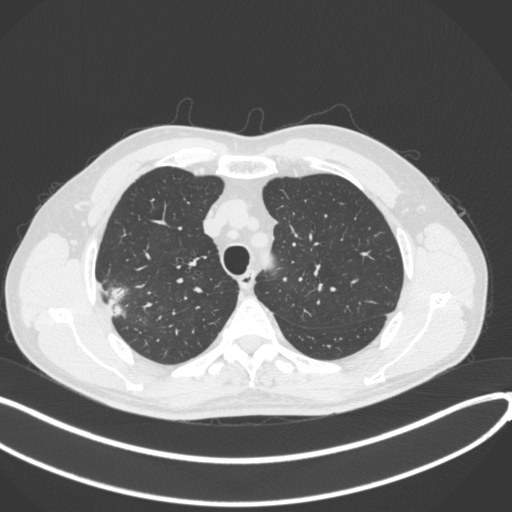
Chest CT, one axial slice; reconstruction kernel B31f; lung window (W 1500 / L -600 HU); 1 mm slice thickness; 512 × 512 image matrix, field of view 400 × 400 mm. Patient: male, 62 years. From the clinical record (not read from this slice): clinical TNM (as recorded): T1c N0 M0.
Outlined on this slice (bounding box drawn by a radiologist):
- lung tumour (recorded histology: adenocarcinoma): bounding box <101,281,126,321> (left, top, right, bottom; pixels)